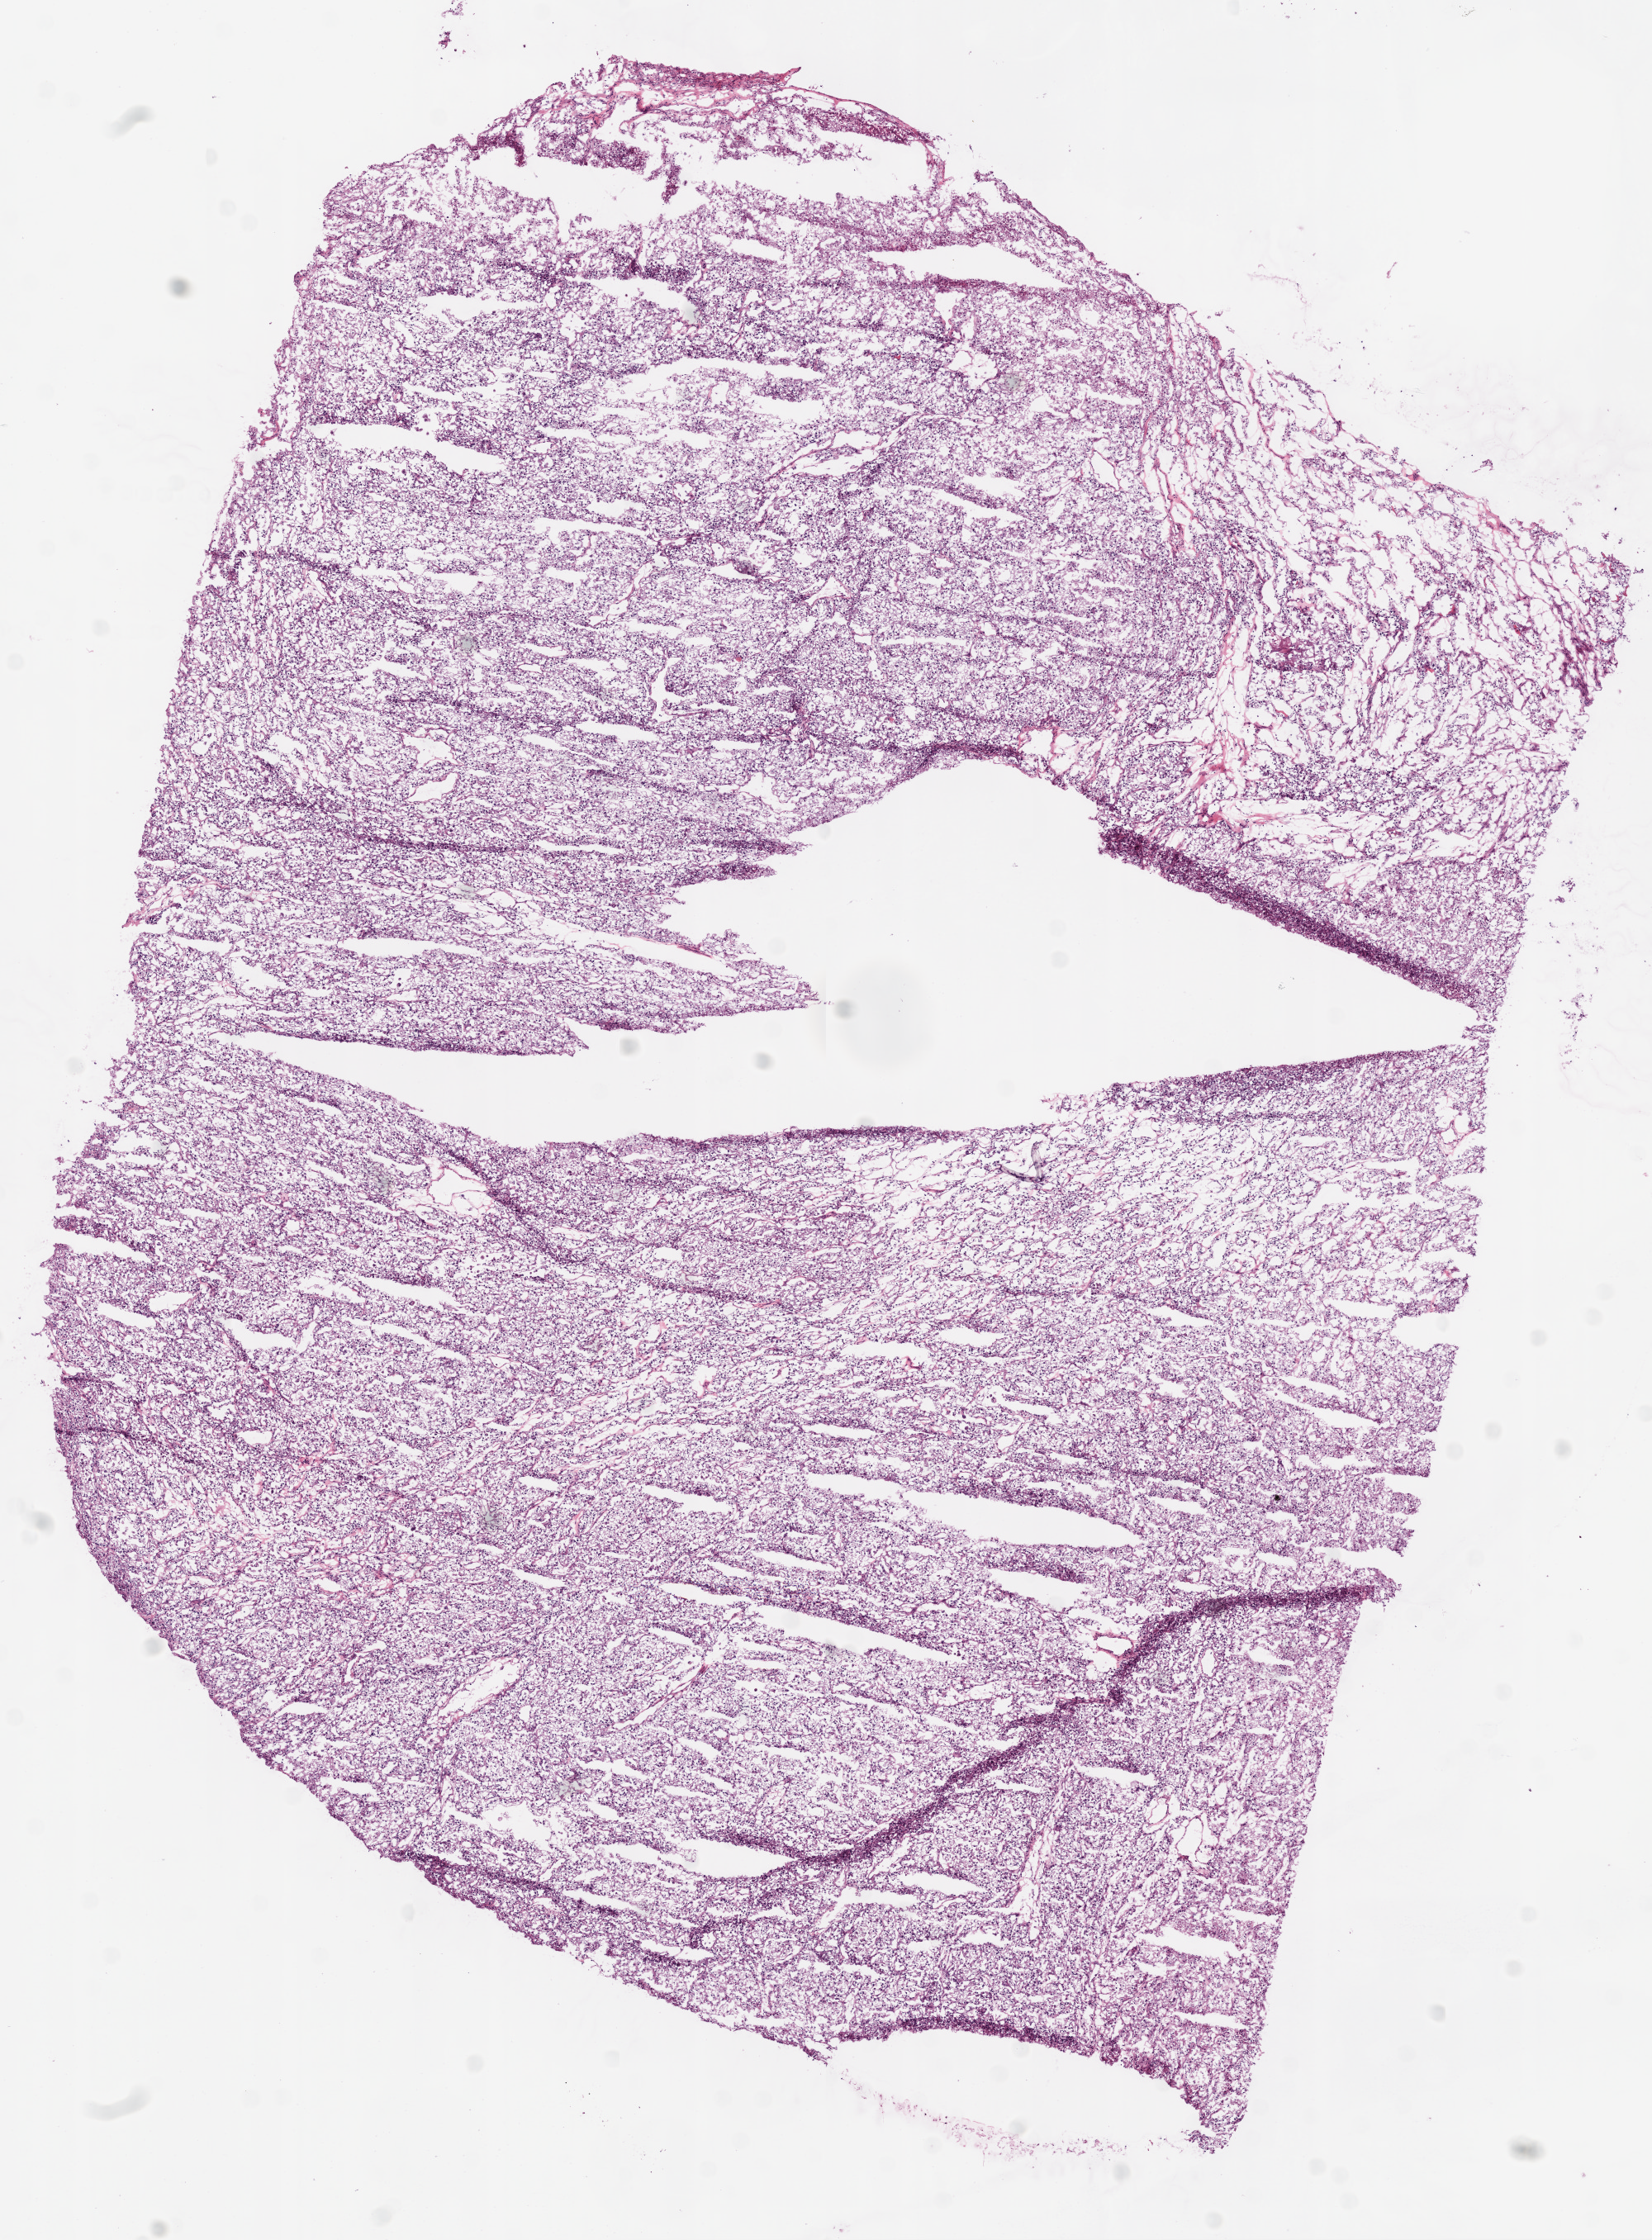
Whole-slide histology image, H&E — whole scanned area (about 8.0 x 10.9 mm, from a 20x scan) shown as a low-resolution overview. Frozen section. Kidney, primary tumour sample. Patient: male, age at initial diagnosis 40 years. Histologic grade: G2 (moderately differentiated). Pathologist review of this section (percent, as recorded): tumour cells 95%, tumour nuclei 80%, normal cells 0%, stromal cells 5%, necrosis 0%.
- pathologic diagnosis: Clear cell adenocarcinoma, NOS
- AJCC pathologic stage: IV (6th edition)